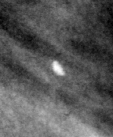
Cropped region of a digitized screen-film mammogram centred on a radiologist-marked abnormality; left breast; MLO view.
Calcifications, morphology lucent center; BI-RADS assessment category 2; benign without callback (not worked up further).